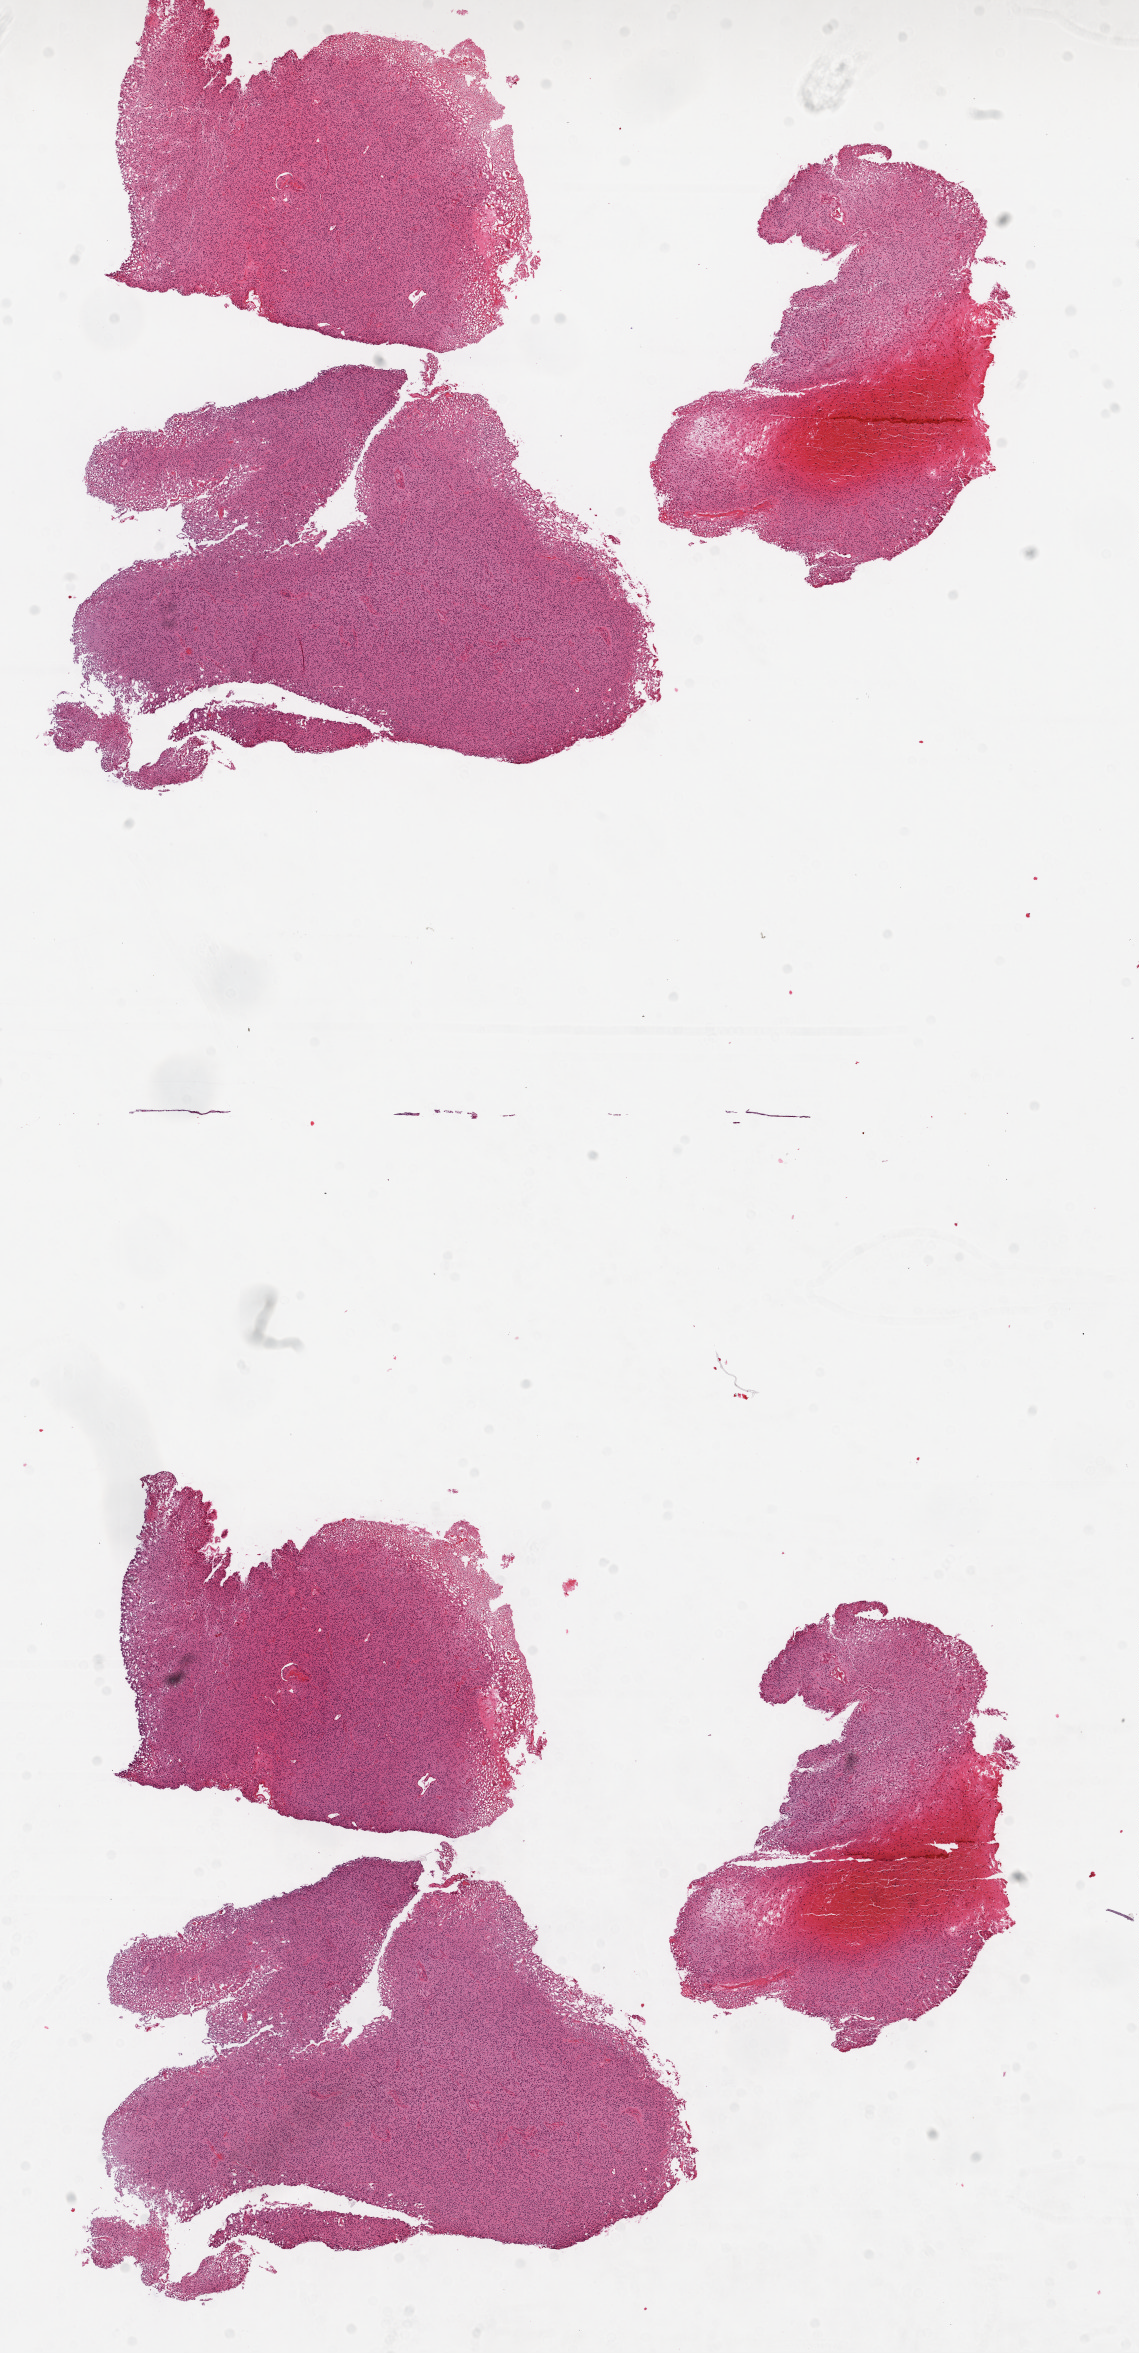
H&E-stained whole-slide image, low-resolution overview of the scanned area, about 9.2 x 19.0 mm (from a 20x scan). Formalin-fixed paraffin-embedded (FFPE) diagnostic section. Primary tumour sample from the brain. Patient: male, age at initial diagnosis 54 years.
Histologic diagnosis: Glioblastoma.